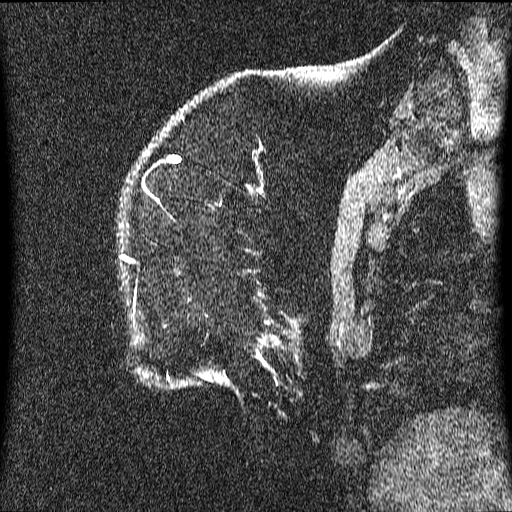
Breast MRI (dynamic contrast-enhanced), one sagittal slice; dynamic contrast-enhanced series, image 2 of 3 at this slice position (ordered by acquisition); 1.5 T; TE 4.2 ms, TR 9.1 ms; 2.2 mm slice thickness; 512 × 512 image matrix, field of view 180 × 180 mm. Female patient, age 52 years.
Outlined on this slice (semi-automatically segmented with operator editing):
- analysis volume of interest (the breast-tissue region the enhancement analysis was run in; not a lesion): bounding box (x1, y1, x2, y2) in pixels: (123, 219, 348, 393)
- tumour enhancement mask (voxels above the 70 % enhancement threshold inside the analysis volume of interest): (258, 355, 266, 364)